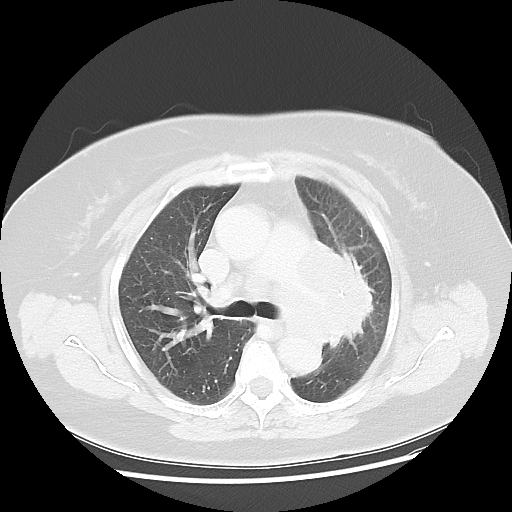
Chest CT, one axial slice. Slice 30 of 49 in the series (ordered by position). Lung window (W 1500 / L -600 HU). 5 mm slice thickness. 512 × 512 image matrix, field of view 374 × 374 mm. Female patient, age 58 years. From the clinical record (not read from this slice): clinical TNM (as recorded): T4 N3 M0; histopathological grade: G3.
Annotated regions visible in this slice (bounding box drawn by a radiologist):
- lung tumour (recorded histology: small cell carcinoma): bounding box (x1, y1, x2, y2) in pixels: (307, 226, 384, 362)